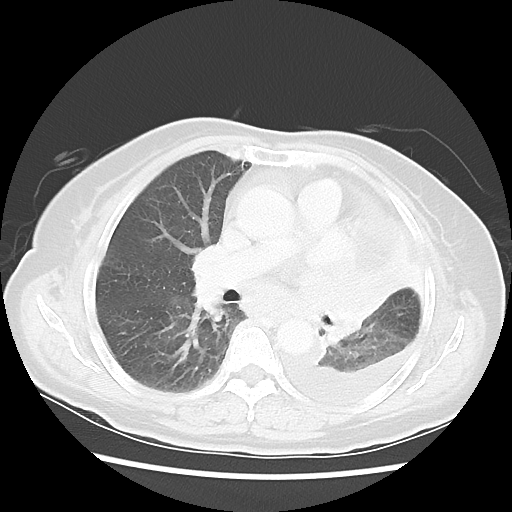
Chest CT, one axial slice; position 31 of 52 along the scan axis; reconstruction kernel LUNG; lung window (W 1500 / L -600 HU); 5 mm slice thickness; 512 × 512 image matrix, field of view 336 × 336 mm. Female patient, age 72 years. Case-level facts recorded for this patient, not image findings: clinical TNM (as recorded): T4 N3 M1b.
Annotated regions visible in this slice (rectangle marked by the reading radiologist):
- lung tumour (recorded histology: large cell carcinoma): bounding box <299,259,398,348> (left, top, right, bottom; pixels)